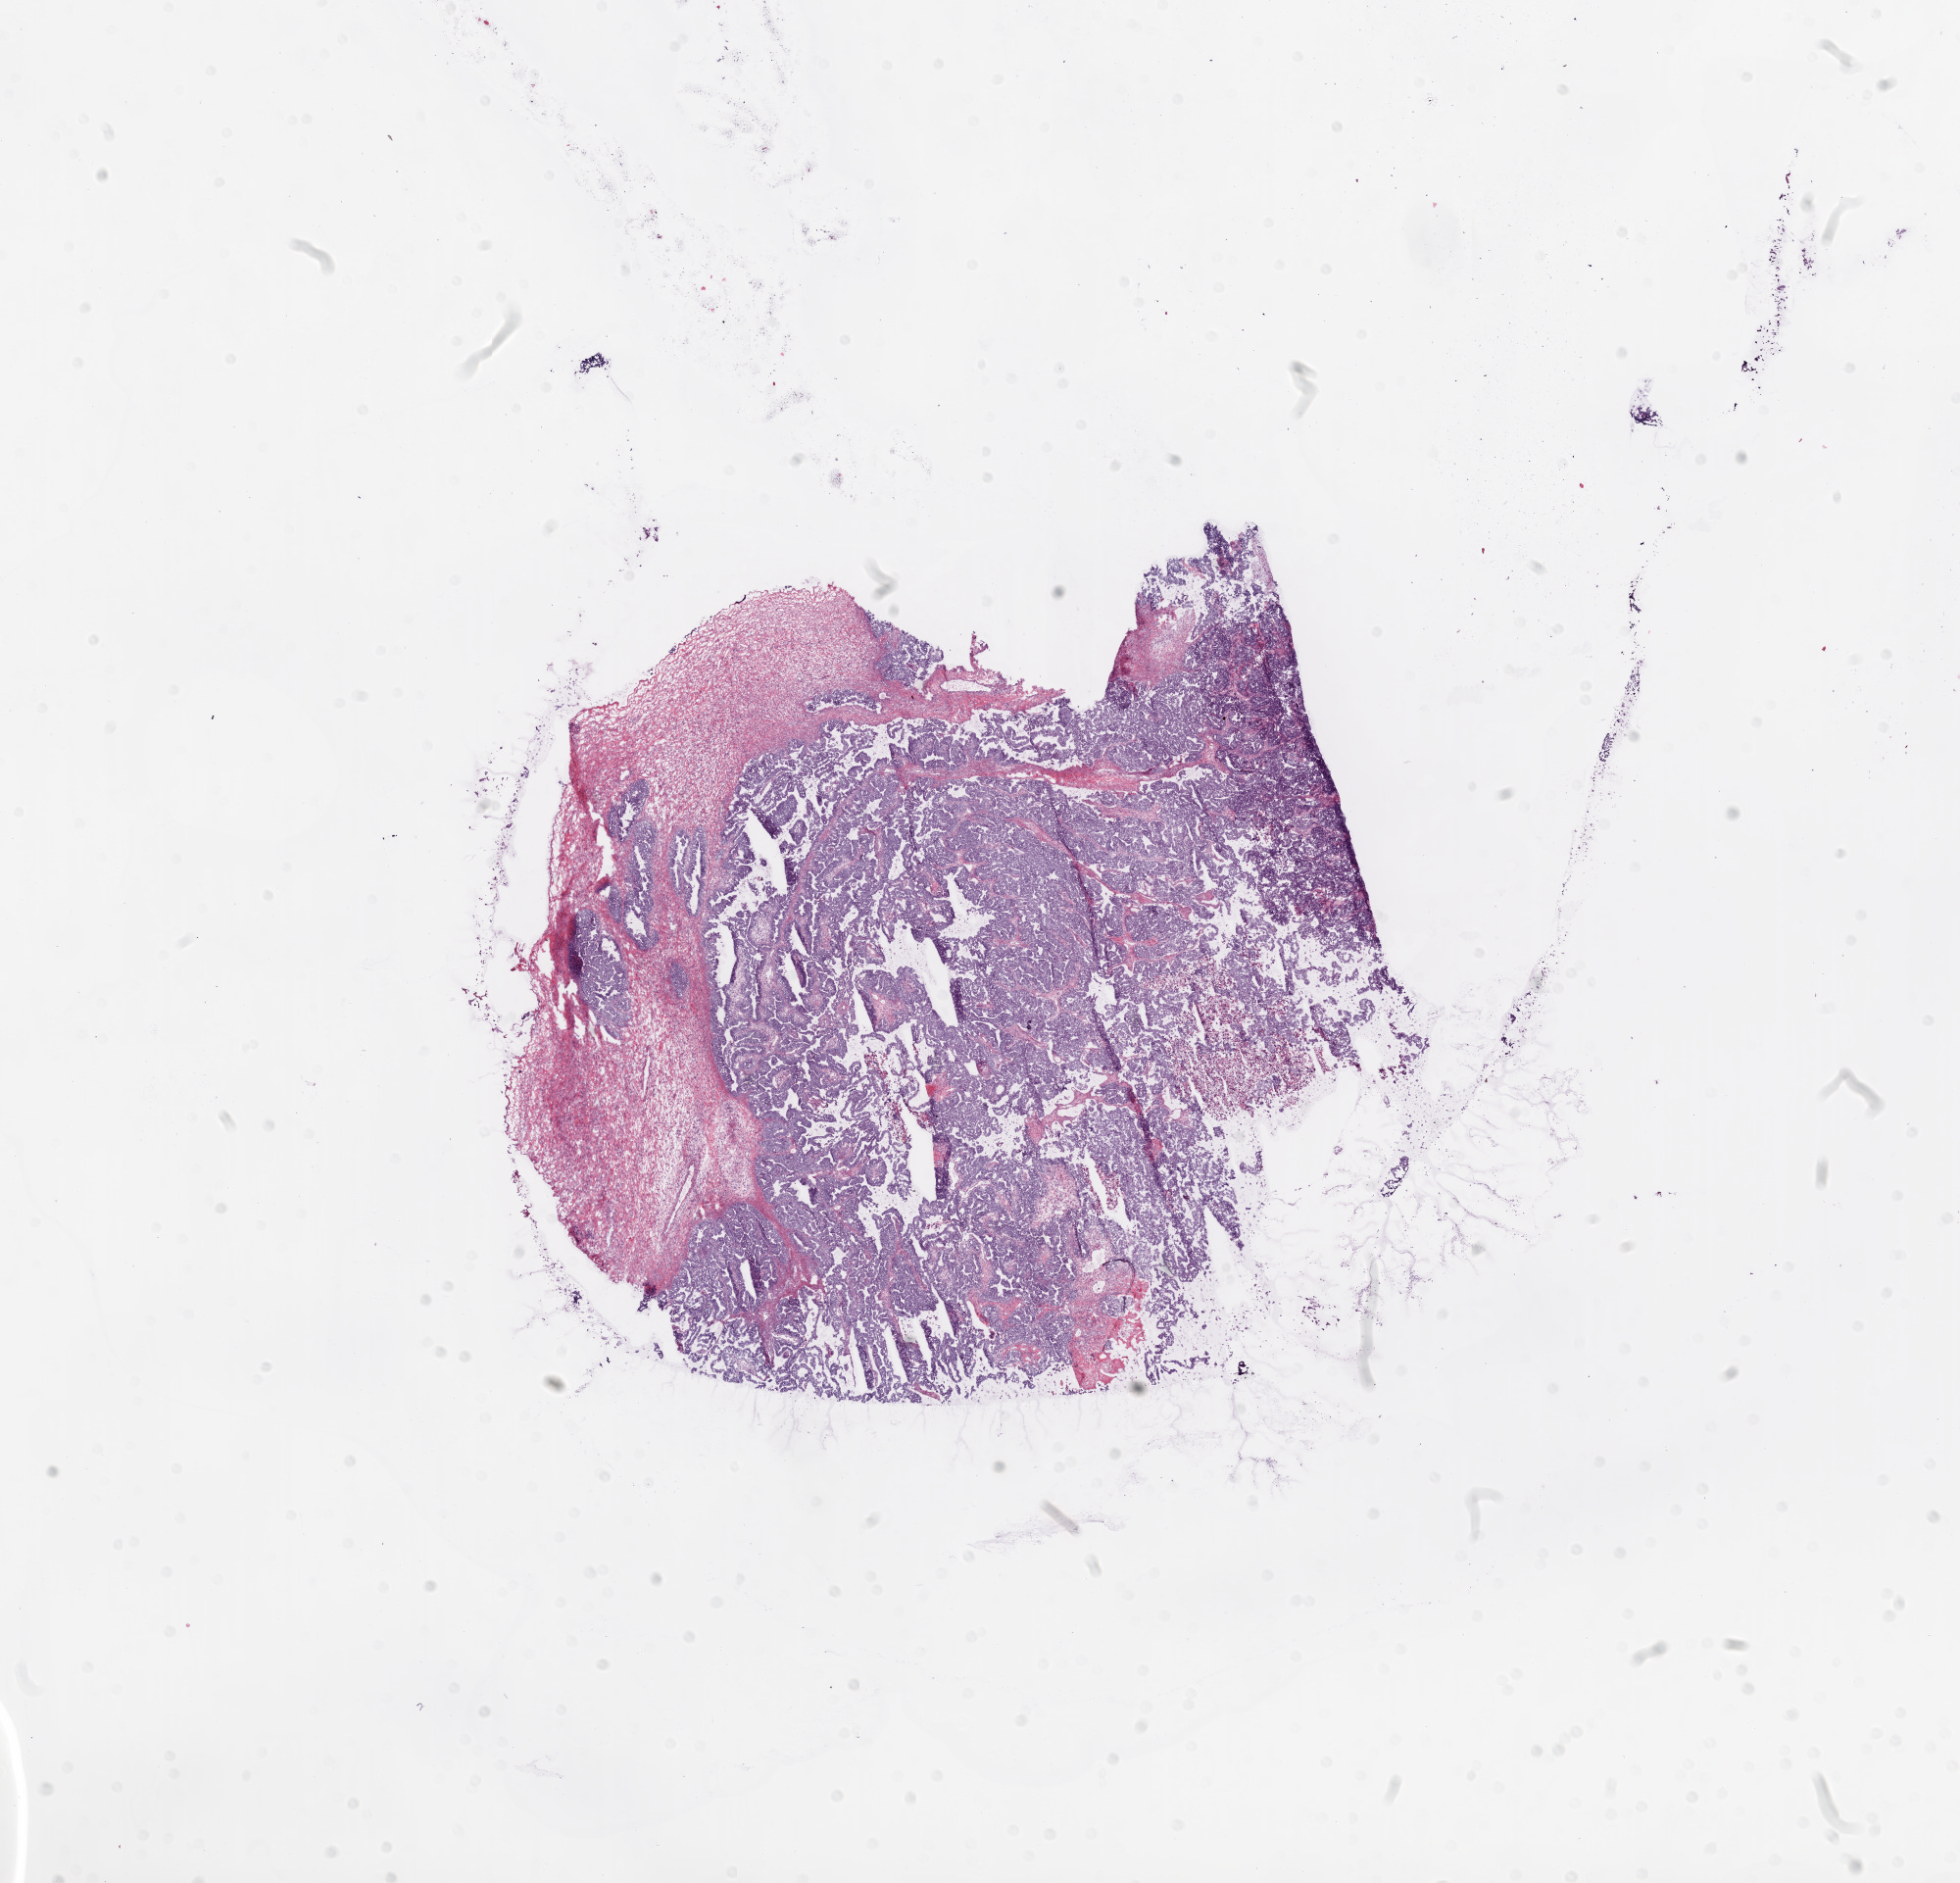
H&E-stained whole-slide image — shown as a low-resolution overview of the whole scanned area (about 16.0 x 15.4 mm, slide scanned at 20x), frozen section from the bottom of the tissue portion, sample: primary tumour, ovary. Female patient; age at initial diagnosis 64 years. Pathologist review of this section (percent, as recorded): tumour cells 80%, tumour nuclei 98%.
Pathologic diagnosis: Serous cystadenocarcinoma, NOS.